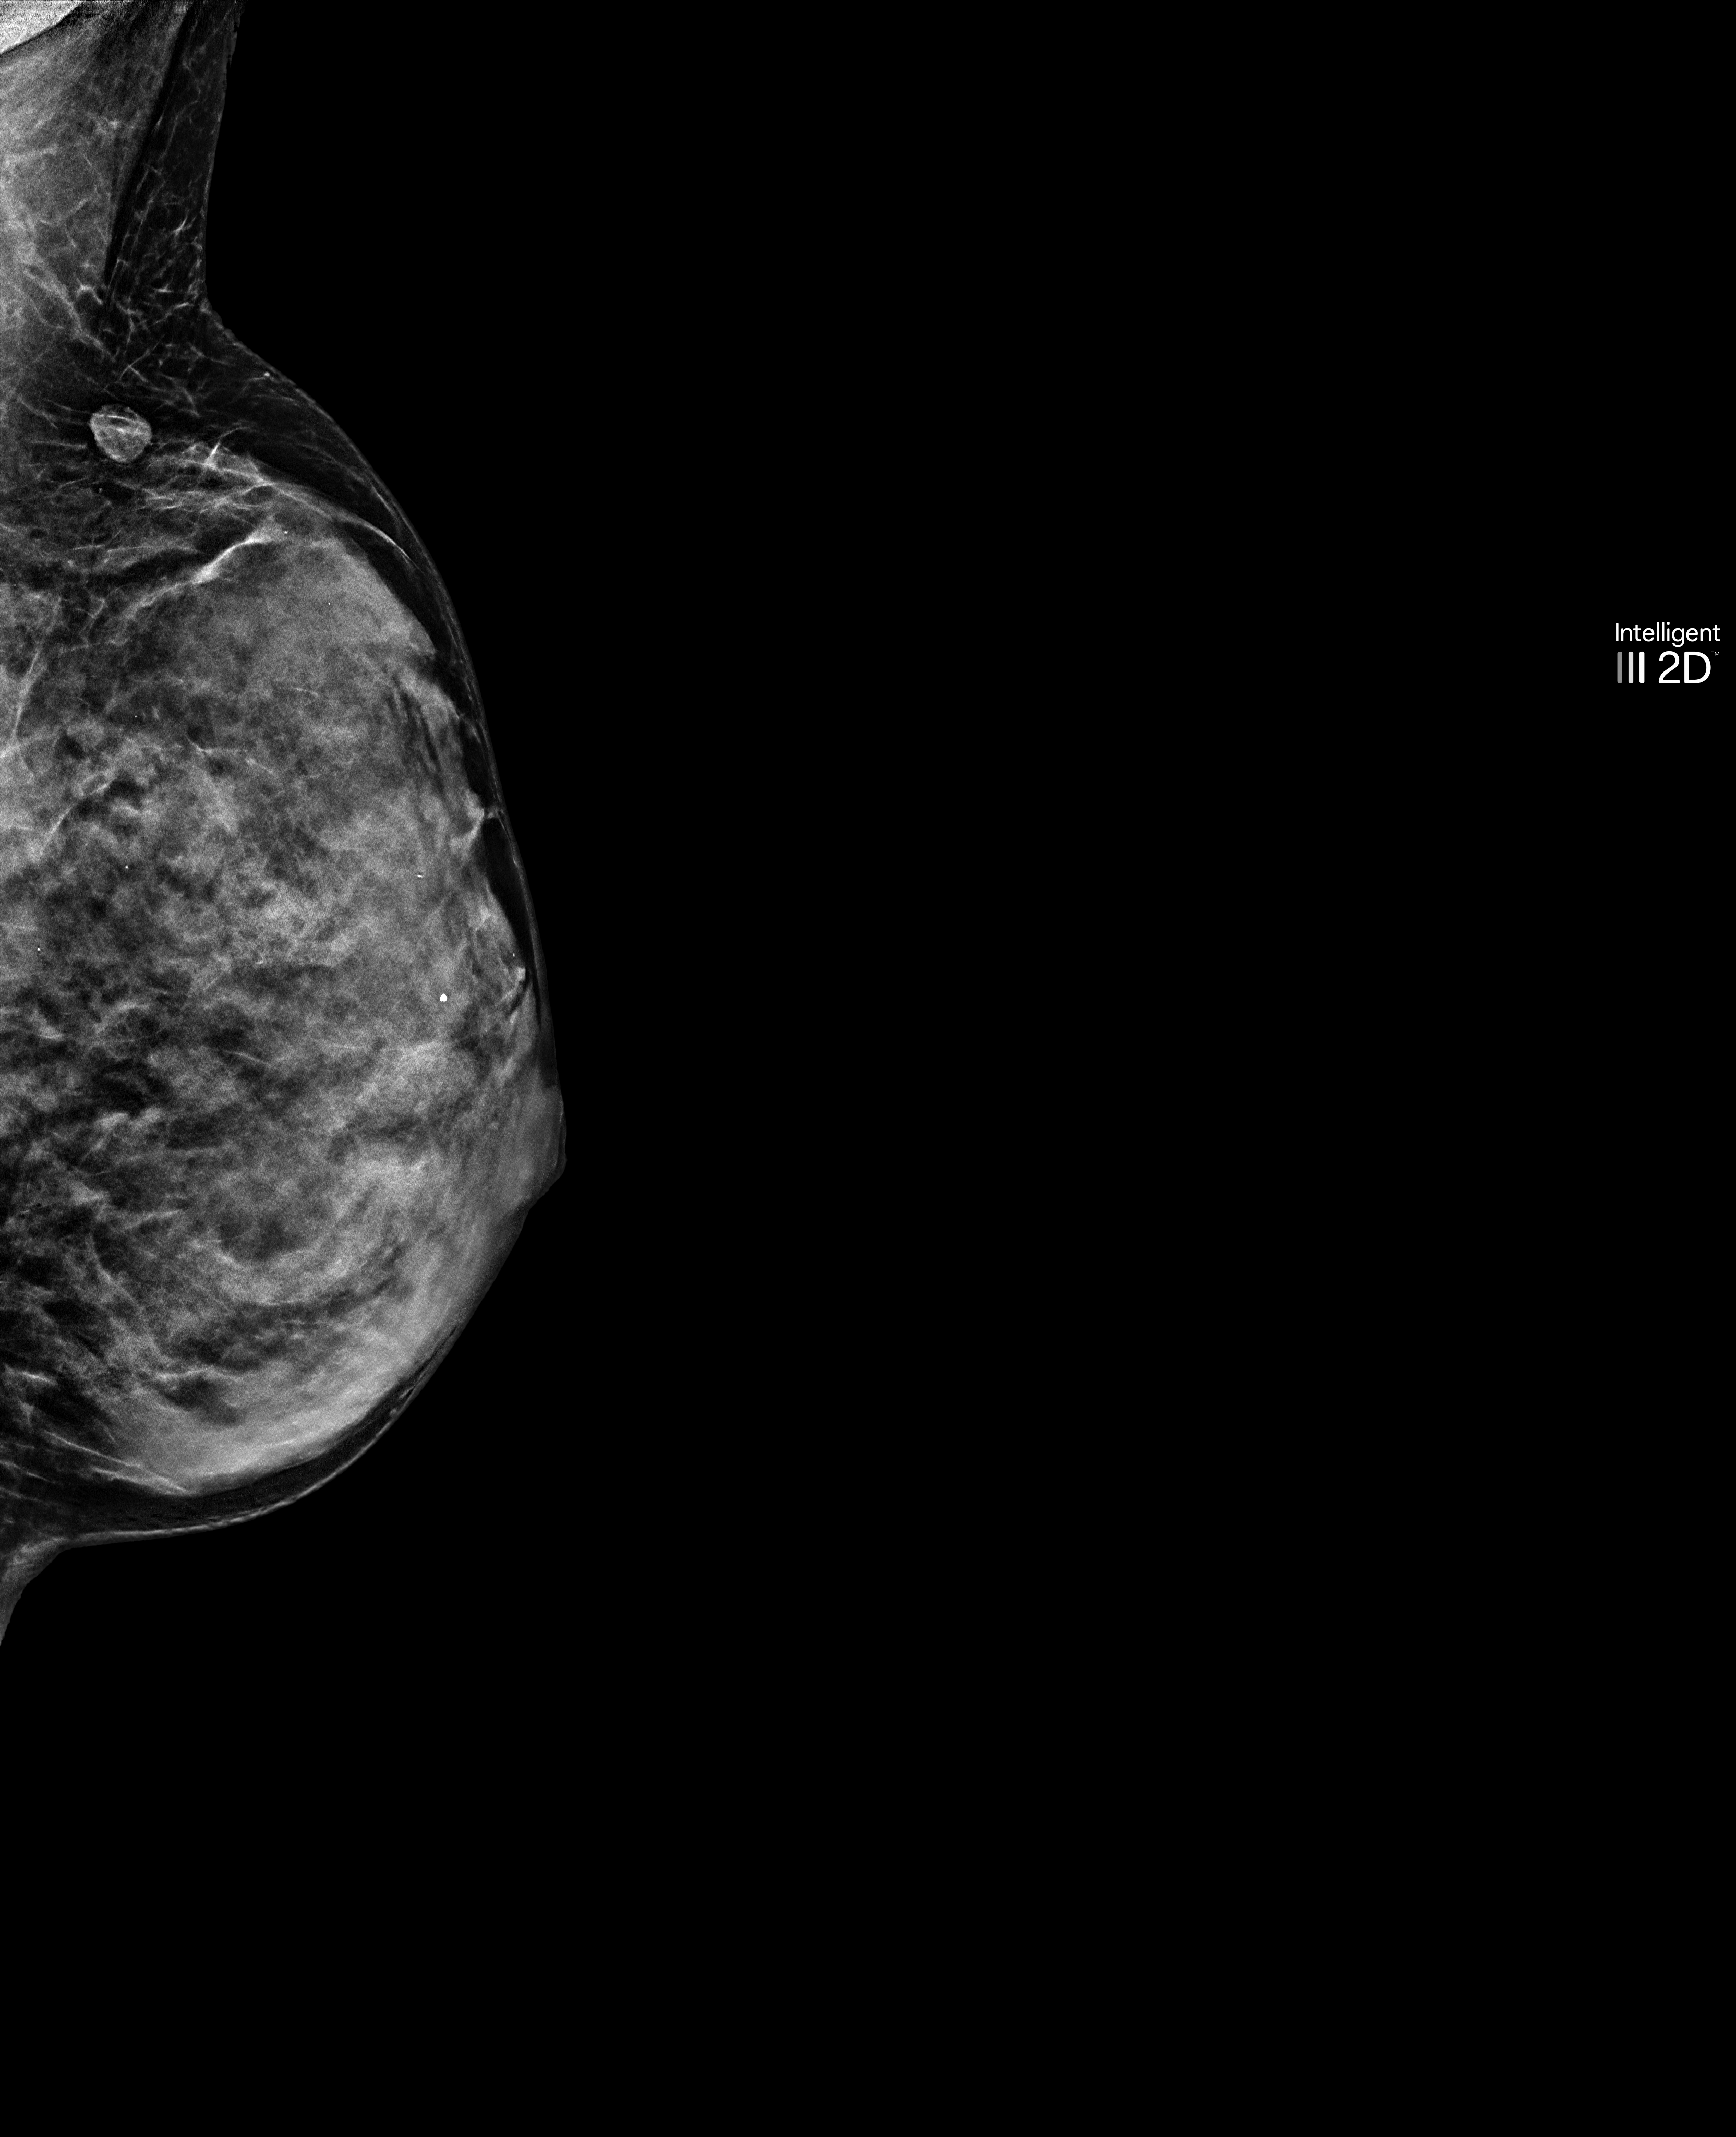
Screening examination. Female patient, age 53 years.
Image type: synthesized 2-D view from tomosynthesis. Breast: left. Projection: medio-lateral oblique projection.